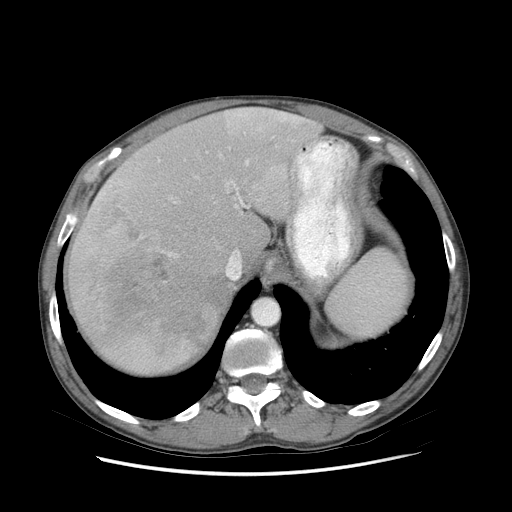
Contrast-enhanced abdominal CT (liver protocol), one axial slice. Position 61 of 89 along the scan axis. Reconstruction kernel STANDARD. Soft-tissue window (W 400 / L 40 HU). 512 × 512 image matrix. From the clinical record (not read from this slice): diagnosis: hepatocellular carcinoma (patient treated with transarterial chemoembolisation; whether this scan precedes or follows treatment is not stated here); TNM stage (as recorded): Stage-IIIB; Child-Pugh class: A; tumour differentiation: moderately differentiated; tumour nodularity: multinodular.
Outlined on this slice (semi-automatic segmentation, software-assisted and operator-edited):
- liver parenchyma outside the tumour (the mass and vessels are separate outlines, so this box may not span the whole liver): bounding box (x1, y1, x2, y2) in pixels: (68, 107, 322, 374)
- mass: (70, 200, 226, 350)
- liver vessels: (96, 110, 301, 260)